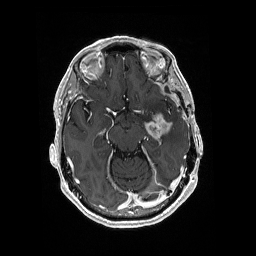
Brain MRI from a brain-tumour surgery series, one axial slice. Position 113 of 176 along the scan axis. T1-weighted post-contrast. 1 mm slice thickness. 256 × 256 image matrix, field of view 256 × 256 mm. Case-level facts recorded for this patient, not image findings: histopathology: Glioblastoma; WHO grade: 4; IDH mutation: no; tumour location: Left Medial Temporal.
Structures marked on this image (outlined manually by an expert reader):
- tumour: box from (x=144, y=113) to (x=173, y=139) px